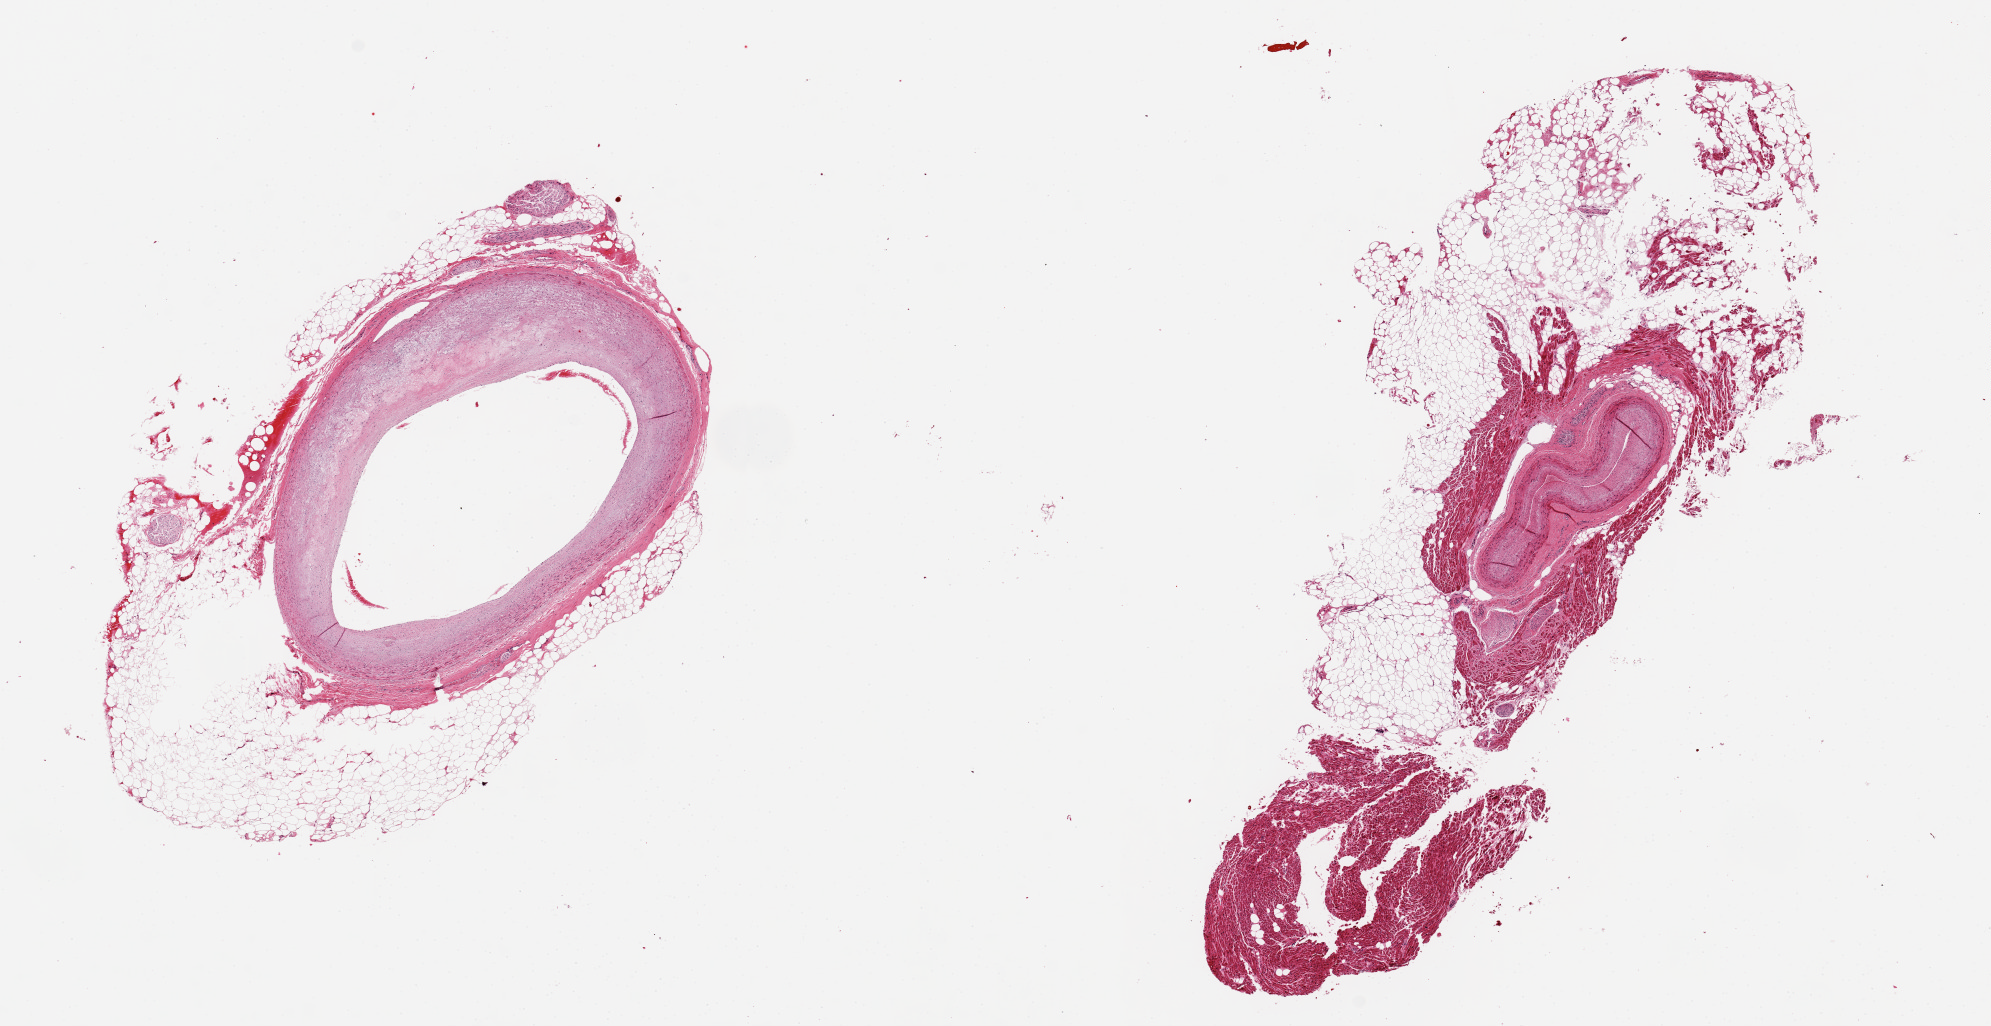
Whole-slide image, hematoxylin and eosin (H&E) stain, shown as a low-resolution overview of the whole scanned area (about 15.8 x 8.1 mm); PAXgene-fixed, paraffin-embedded tissue; sampled site (target tissue): coronary artery; tissue donor sample. Female donor.
Review note (as recorded): 2 aliquots, 1 3.5mm d, one is fat and minute vessel, unacceptable for use.